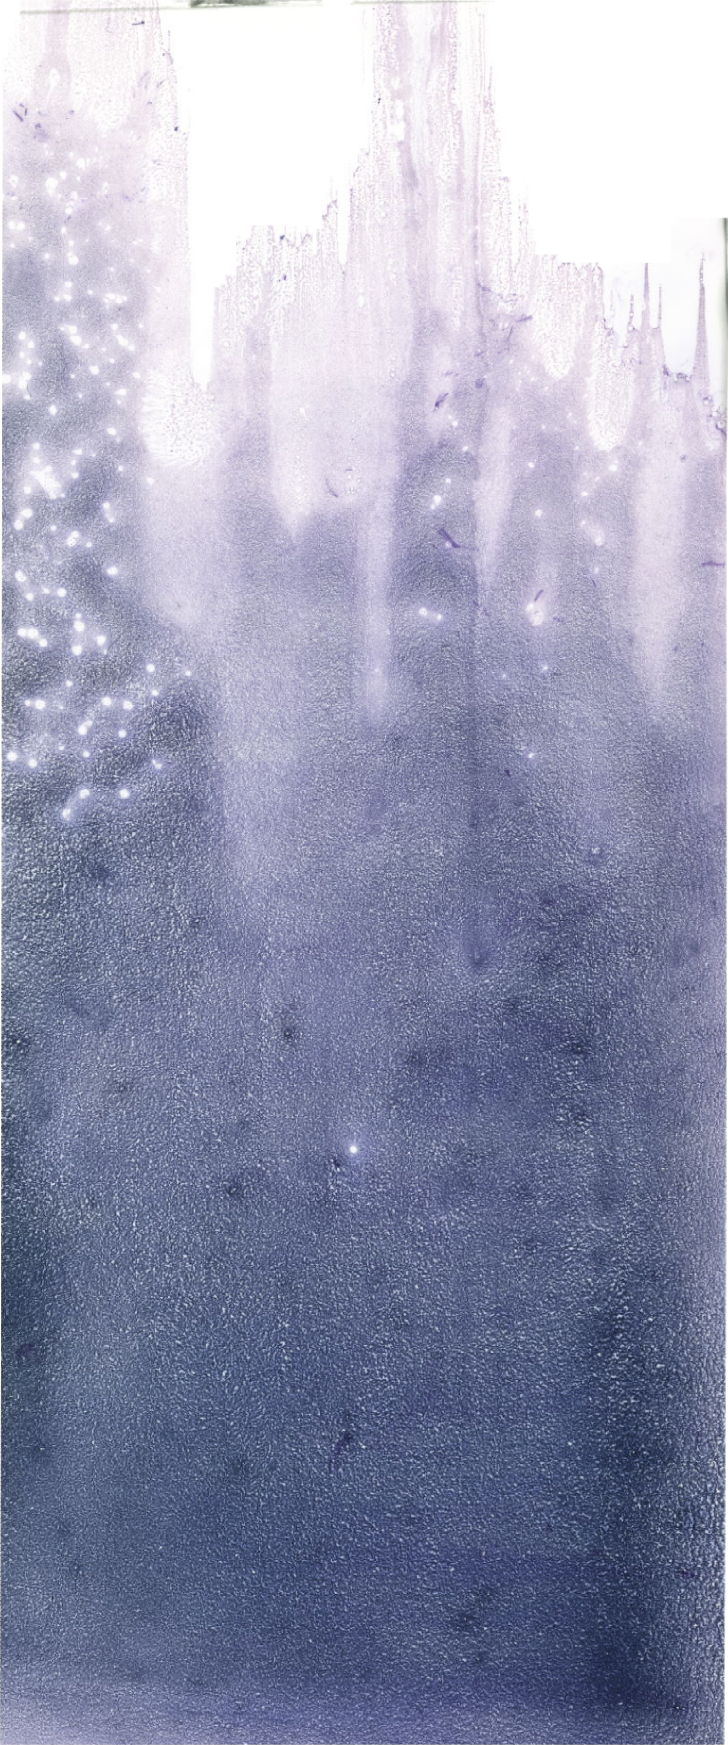
Bone marrow aspirate smear, May-Grünwald-Giemsa (MGG) stain, whole-slide image, whole scanned area (about 20.6 x 49.5 mm) shown as a low-resolution overview. Female patient.